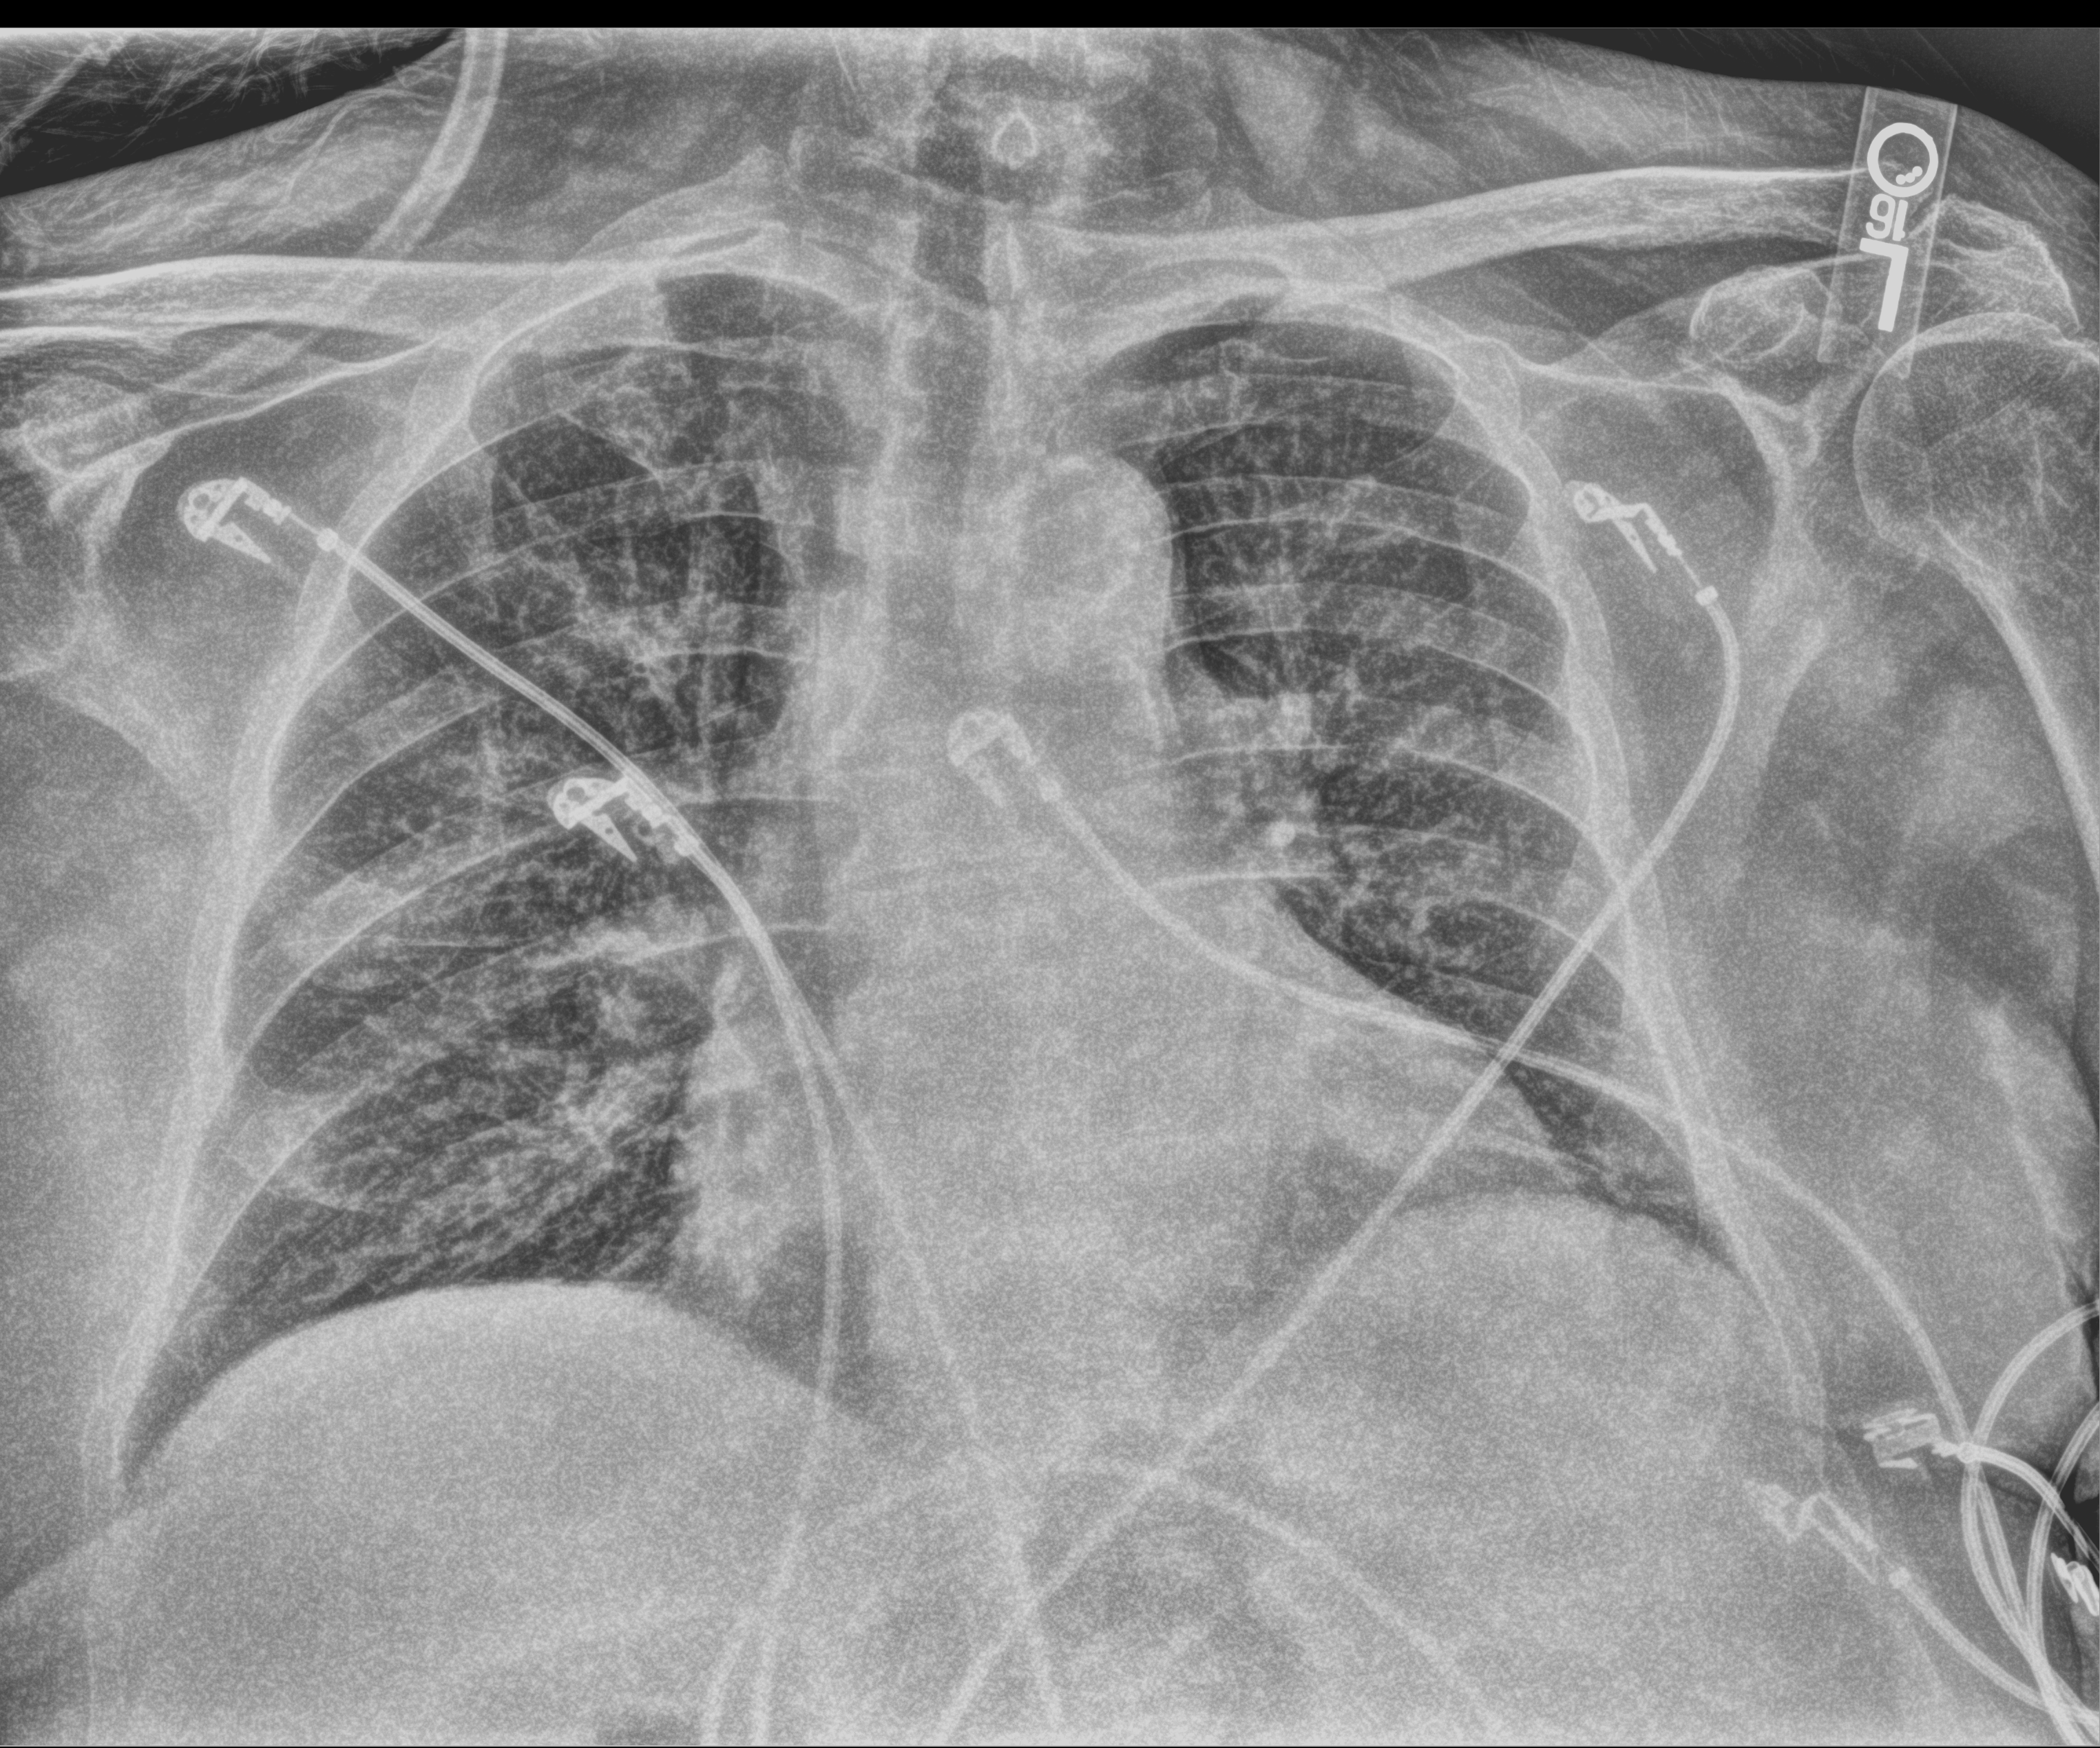
Bedside chest radiograph (computed radiography), anteroposterior (AP) projection. Patient hospitalised with COVID-19; male, aged 75–90 years.
From the hospital-stay record, not from the radiograph (when in the stay this image was taken is not recorded): COPD (admission record): no; mechanically ventilated during this hospital stay: no; admitted to intensive care during this hospital stay: no.